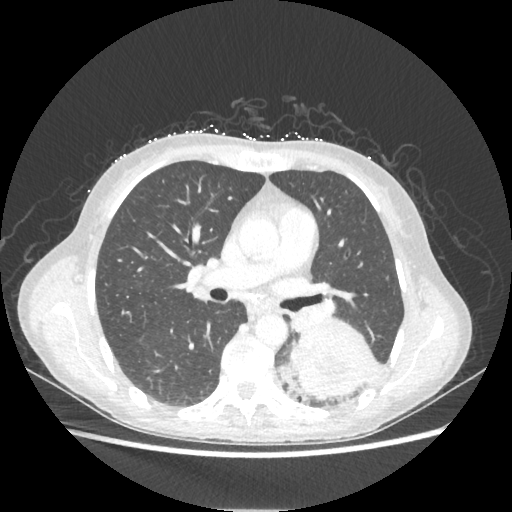
Chest CT, one axial slice; slice 125 of 221 in the series (ordered by position); lung window (W 1500 / L -600 HU); 512 × 512 image matrix. Patient: female, 53 years. Case-level facts recorded for this patient, not image findings: clinical TNM (as recorded): T3 N0 M0.
Annotated regions visible in this slice (bounding box drawn by a radiologist):
- lung tumour (recorded histology: adenocarcinoma): bounding box <290,318,373,398> (left, top, right, bottom; pixels)